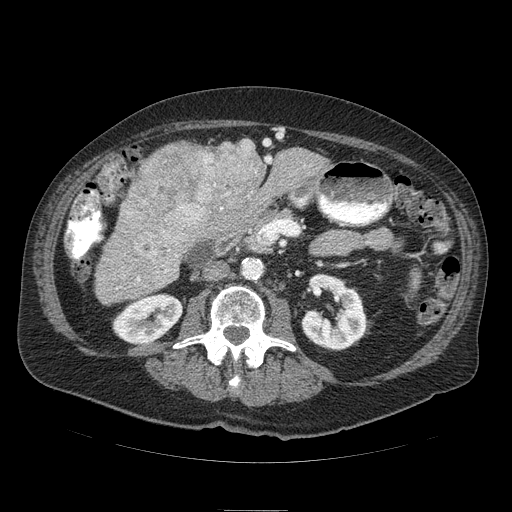
Contrast-enhanced abdominal CT (liver protocol), one axial slice. Slice 28 of 103 in the series (ordered by position). 120 kVp. Soft-tissue window (W 400 / L 40 HU). 512 × 512 image matrix, field of view 440 × 440 mm. From the clinical record (not read from this slice): diagnosis: hepatocellular carcinoma (patient treated with transarterial chemoembolisation; whether this scan precedes or follows treatment is not stated here); TNM stage (as recorded): Stage-IIIA; Child-Pugh class: B; tumour differentiation: well differentiated; tumour nodularity: multinodular.
Annotated regions visible in this slice (semi-automatic segmentation, software-assisted and operator-edited):
- liver parenchyma outside the tumour (the mass and vessels are separate outlines, so this box may not span the whole liver): bounding box [x1, y1, x2, y2] px = [96, 138, 328, 294]
- mass: [123, 139, 266, 275]
- liver vessels: [137, 157, 271, 281]